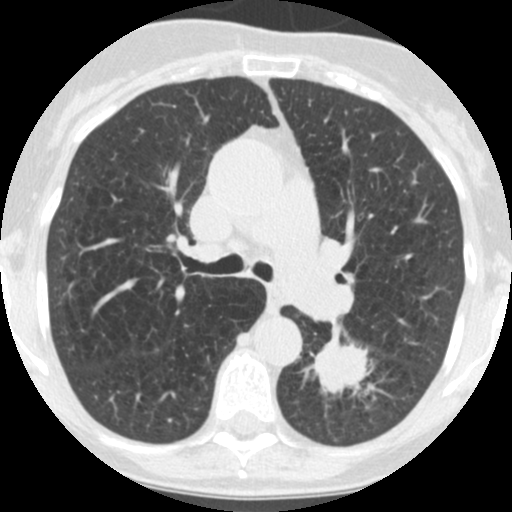
Low-dose screening chest CT, axial slice. Third annual screen. Lung window (W 1500 / L -600 HU). 512 × 512 image matrix. Female participant, aged 71 years at enrolment.
Expert reader's lesion annotation, bounding box [x1, y1, x2, y2] px = [304, 326, 384, 410]. The screening reader recorded 2 non-calcified nodules or masses ≥4 mm on this exam (left lower lobe, left lower lobe); which of them this box marks is not recorded. Official screen result: positive, other. Later outcome: lung cancer diagnosed 26 days after this screen — squamous cell carcinoma, NOS, left lower lobe, poorly differentiated (G3), stage IB (AJCC 6th edition), 40 mm at pathology.